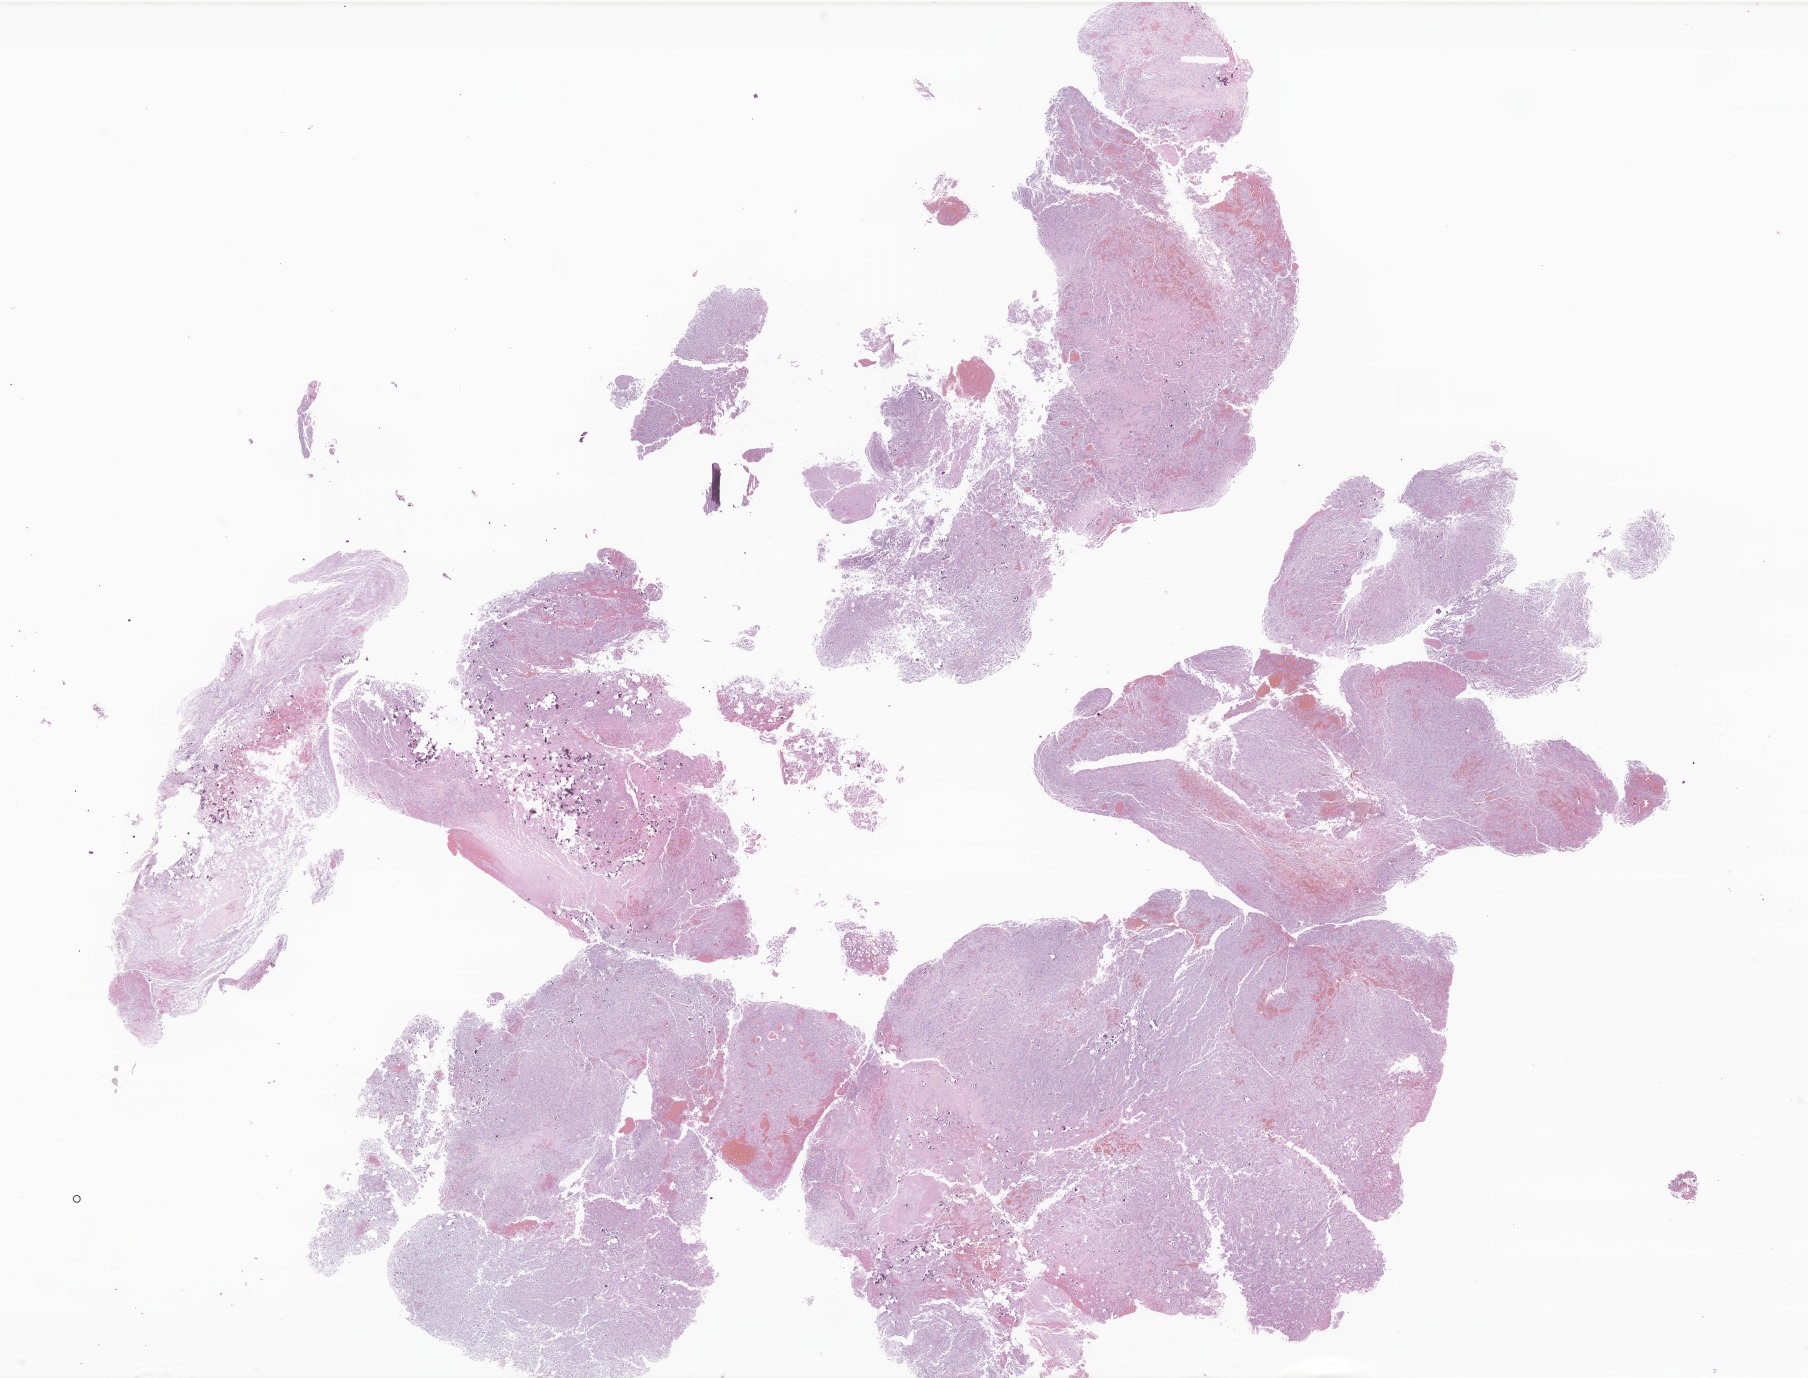
Haematoxylin and eosin whole-slide image of tumor tissue from the brain — whole scanned area (about 30.5 x 23.2 mm) shown as a low-resolution overview, FFPE section. Patient: male, age 201 months (16 years 9 months).
Diagnosis: Tumor cells, uncertain whether benign or malignant.